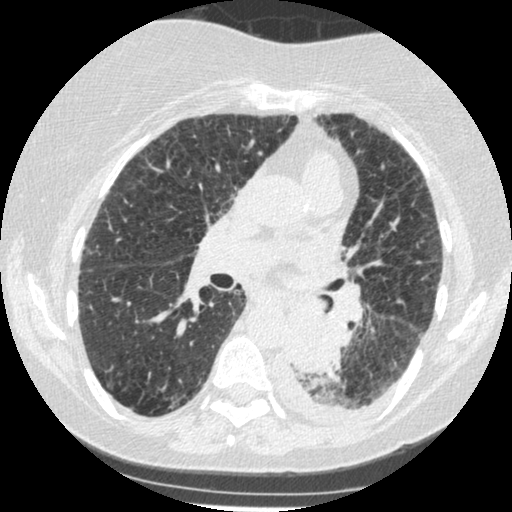
Low-dose screening chest CT, axial slice, third annual screen, lung window (W 1500 / L -600 HU), 1.25 mm slice thickness, slice 205 of 341 in the series. Female participant, aged 60 years at enrolment. Former smoker at enrolment.
Expert reader's lesion annotation, bounding box <271,306,342,374> (left, top, right, bottom; pixels). The exam's reader record, not a measurement of the box and not confirmed to be the same lesion: non-calcified nodule or mass ≥4 mm, left lower lobe, 54 × 38 mm, smooth margins, soft tissue attenuation, pre-existing on the prior screen: yes; interval growth: yes. Later outcome: lung cancer diagnosed 15 days after this screen — small cell carcinoma, NOS, left lower lobe, undifferentiated (G4), stage IV (AJCC 6th edition), 69 mm at pathology.